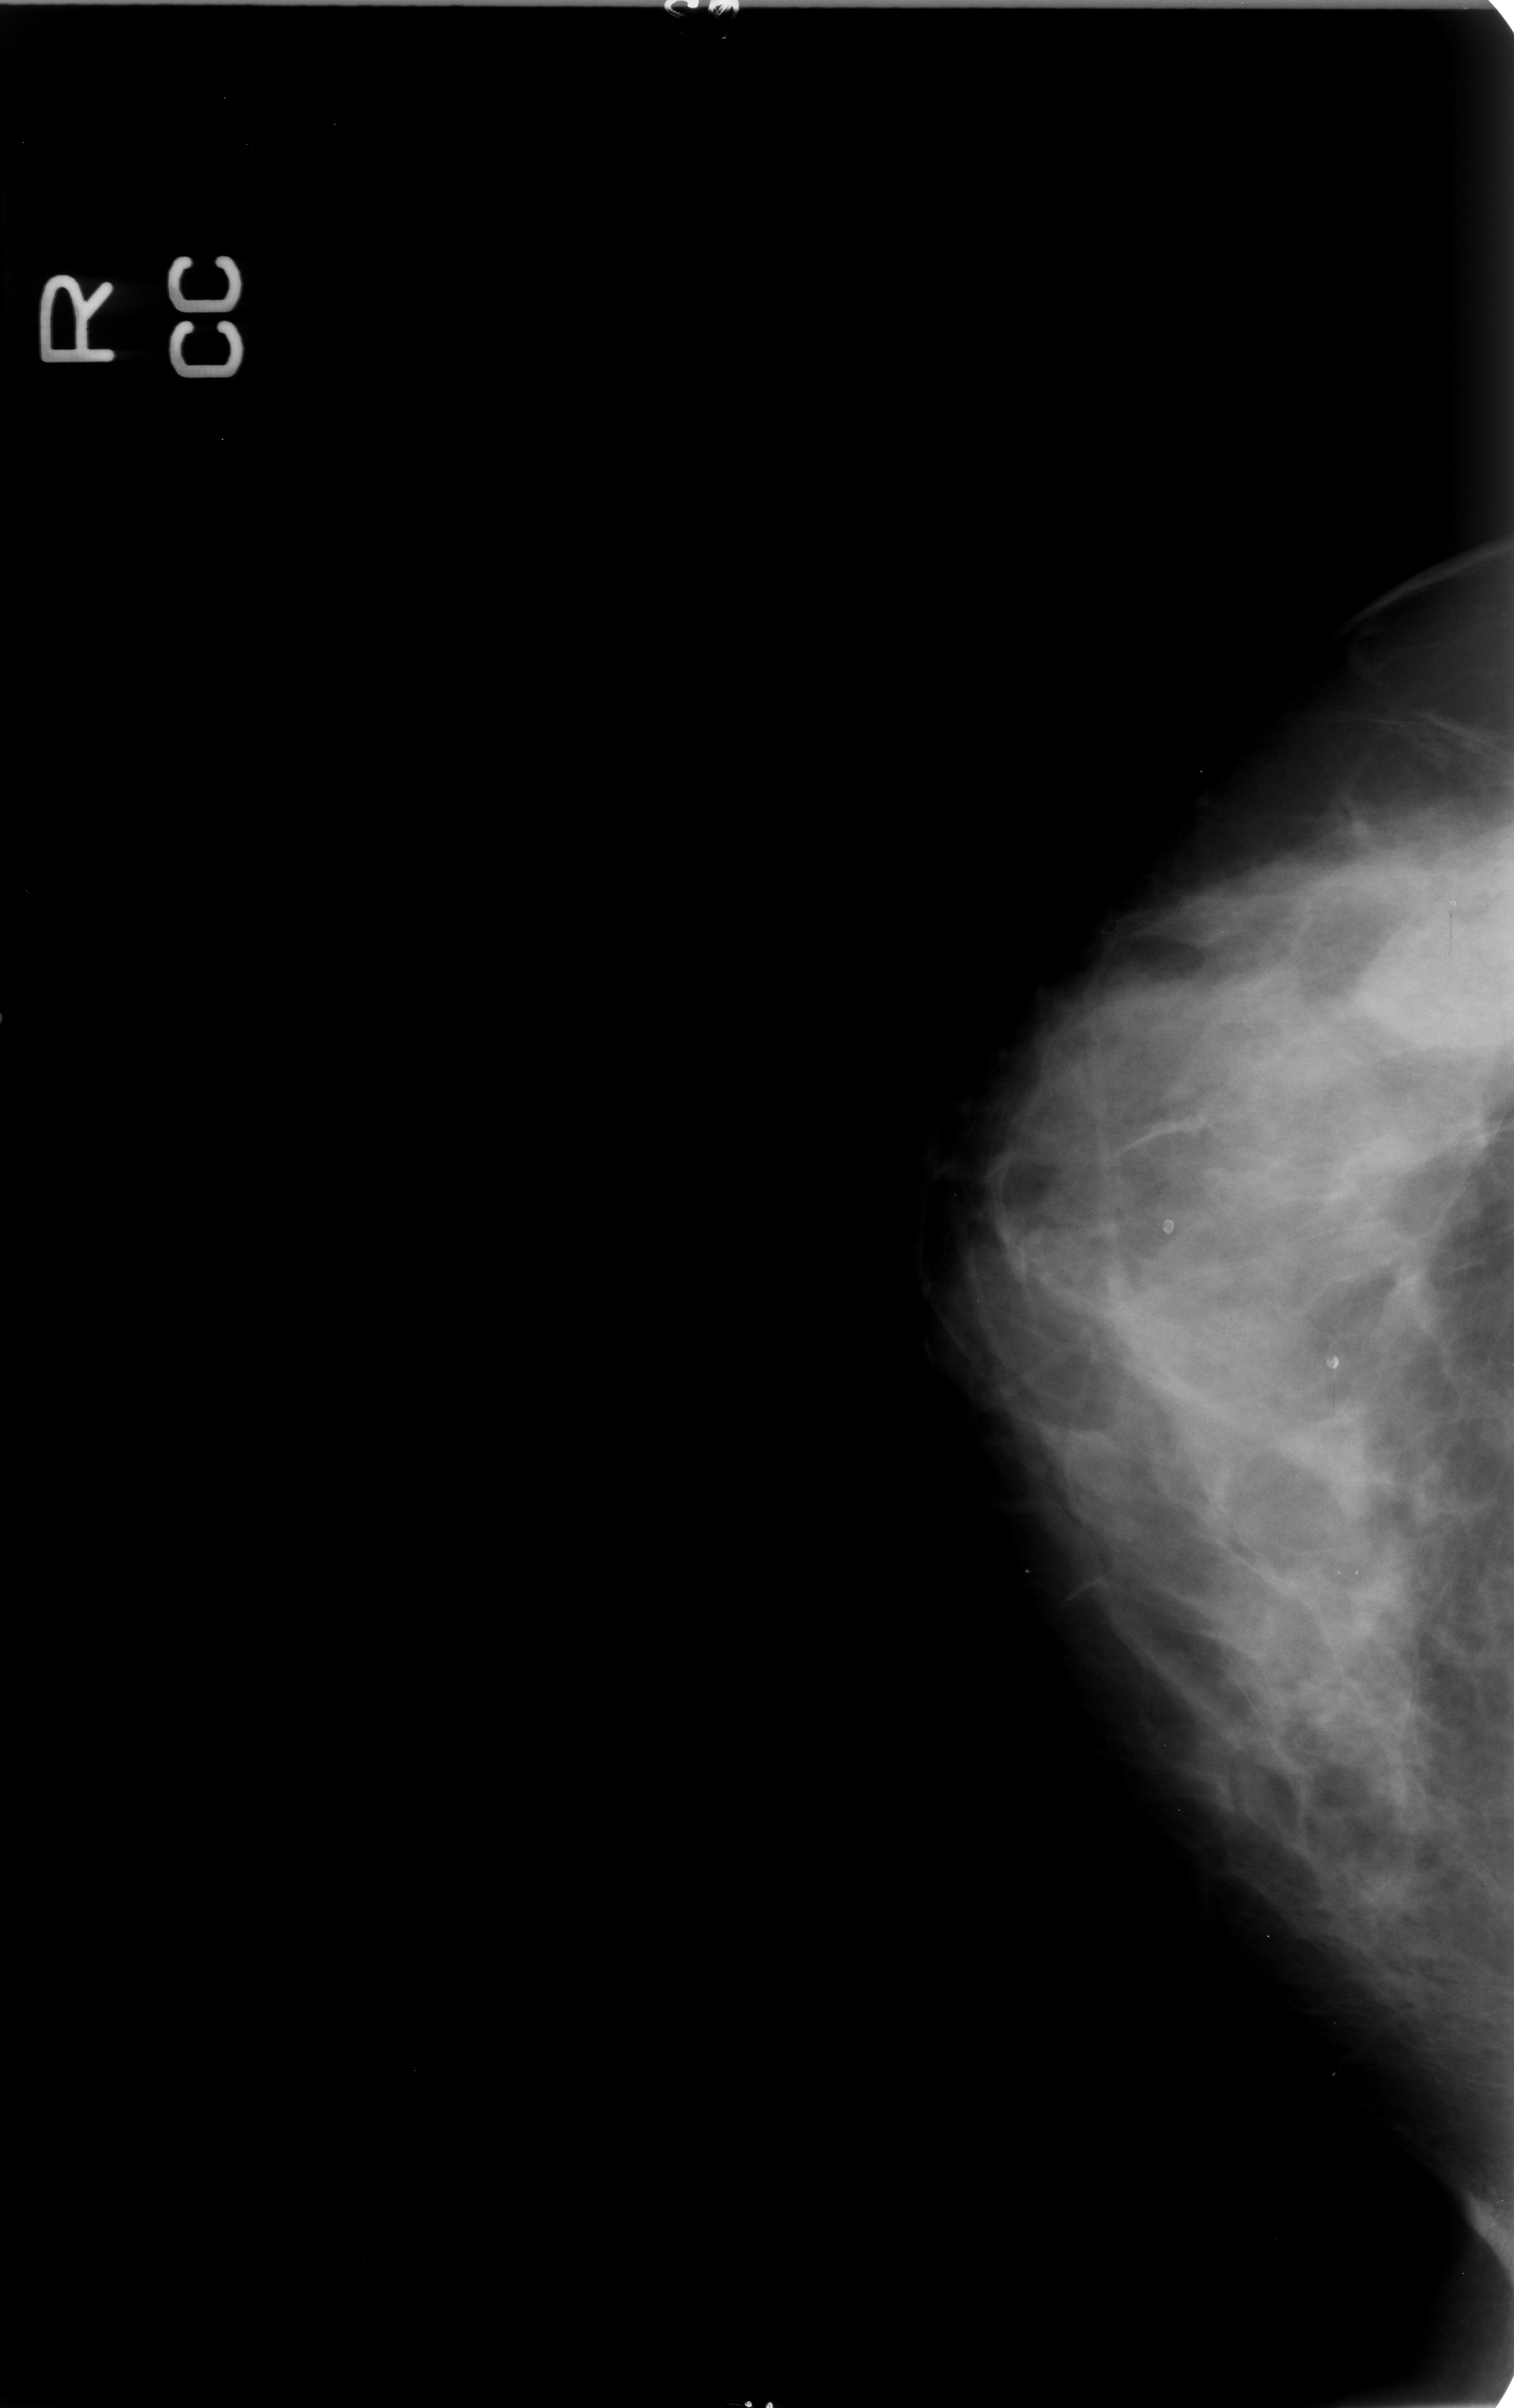
Digitized screen-film mammogram; right breast; CC view.
Radiologist-marked abnormalities on this image: Finding 1 of 3: calcifications, morphology round and regular / lucent centered; BI-RADS assessment category 2; subtlety rating 3 on a 1 (subtle) to 5 (obvious) scale; benign; no additional work-up was recommended (benign without callback). Finding 2 of 3: calcifications, morphology round and regular / lucent centered; BI-RADS assessment category 2; benign without callback (not worked up further). Finding 3 of 3: calcifications, morphology round and regular / lucent centered; BI-RADS assessment category 2; benign without callback (not worked up further).